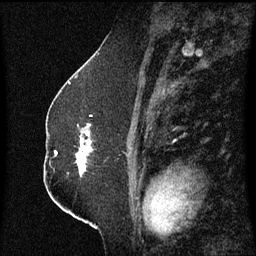
Breast MRI (dynamic contrast-enhanced), one sagittal slice; slice 35 of 60 in the series (ordered by position); dynamic contrast-enhanced series, image 2 of 3 at this slice position (ordered by acquisition); 1.5 T; TE 4.2 ms, TR 8.4 ms; 2.3 mm slice thickness; 256 × 256 image matrix. Patient: female, 52 years. From the clinical record (not read from this slice): setting: breast cancer imaged before/during neoadjuvant chemotherapy; receptor status: HR-positive, HER2-negative.
Outlined on this slice (semi-automatically segmented with operator editing):
- analysis volume of interest (the breast-tissue region the enhancement analysis was run in; not a lesion): box from (x=77, y=116) to (x=107, y=179) px
- tumour enhancement mask (voxels above the 70 % enhancement threshold inside the analysis volume of interest): (x=77, y=124)–(x=92, y=175)